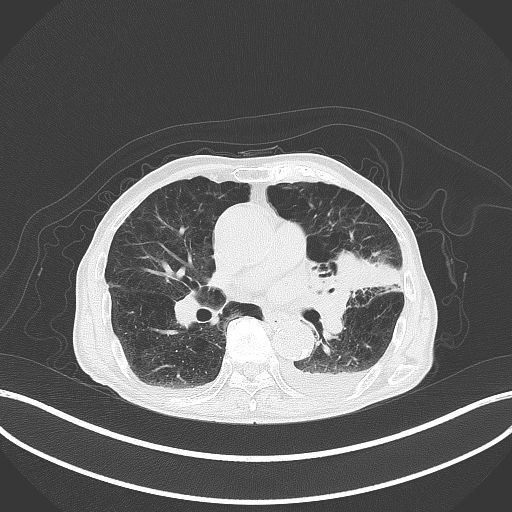
Chest CT, one axial slice; slice 188 of 227 in the series (ordered by position); reconstruction kernel B70f; 120 kVp; lung window (W 1500 / L -600 HU); 3 mm slice thickness; 512 × 512 image matrix, field of view 400 × 400 mm. Male patient, age 90 years or older. From the clinical record (not read from this slice): clinical TNM (as recorded): T2b N1 M0.
Annotated regions visible in this slice (bounding box drawn by a radiologist):
- lung tumour (recorded histology: squamous cell carcinoma): bounding box (x1, y1, x2, y2) in pixels: (333, 250, 402, 296)